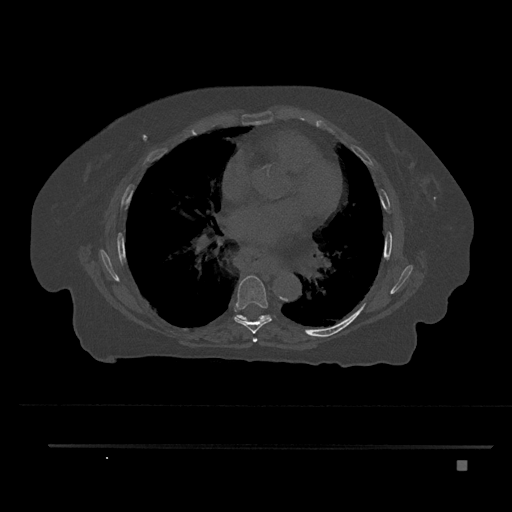
CT including the spine, one axial slice; slice 479 of 797 in the series (ordered by position); bone window (W 1800 / L 400 HU); 0.5 mm slice thickness; 512 × 512 image matrix, field of view 437 × 437 mm. Female patient, age 76 years. Case-level facts recorded for this patient, not image findings: primary cancer: lung.
Outlined on this slice (semi-automatic segmentation, software-assisted and operator-edited):
- T6 vertebra: bounding box <253,337,258,343> (left, top, right, bottom; pixels)
- T7 vertebra: <234,275,272,334>
- T8 vertebra: <235,315,270,321>